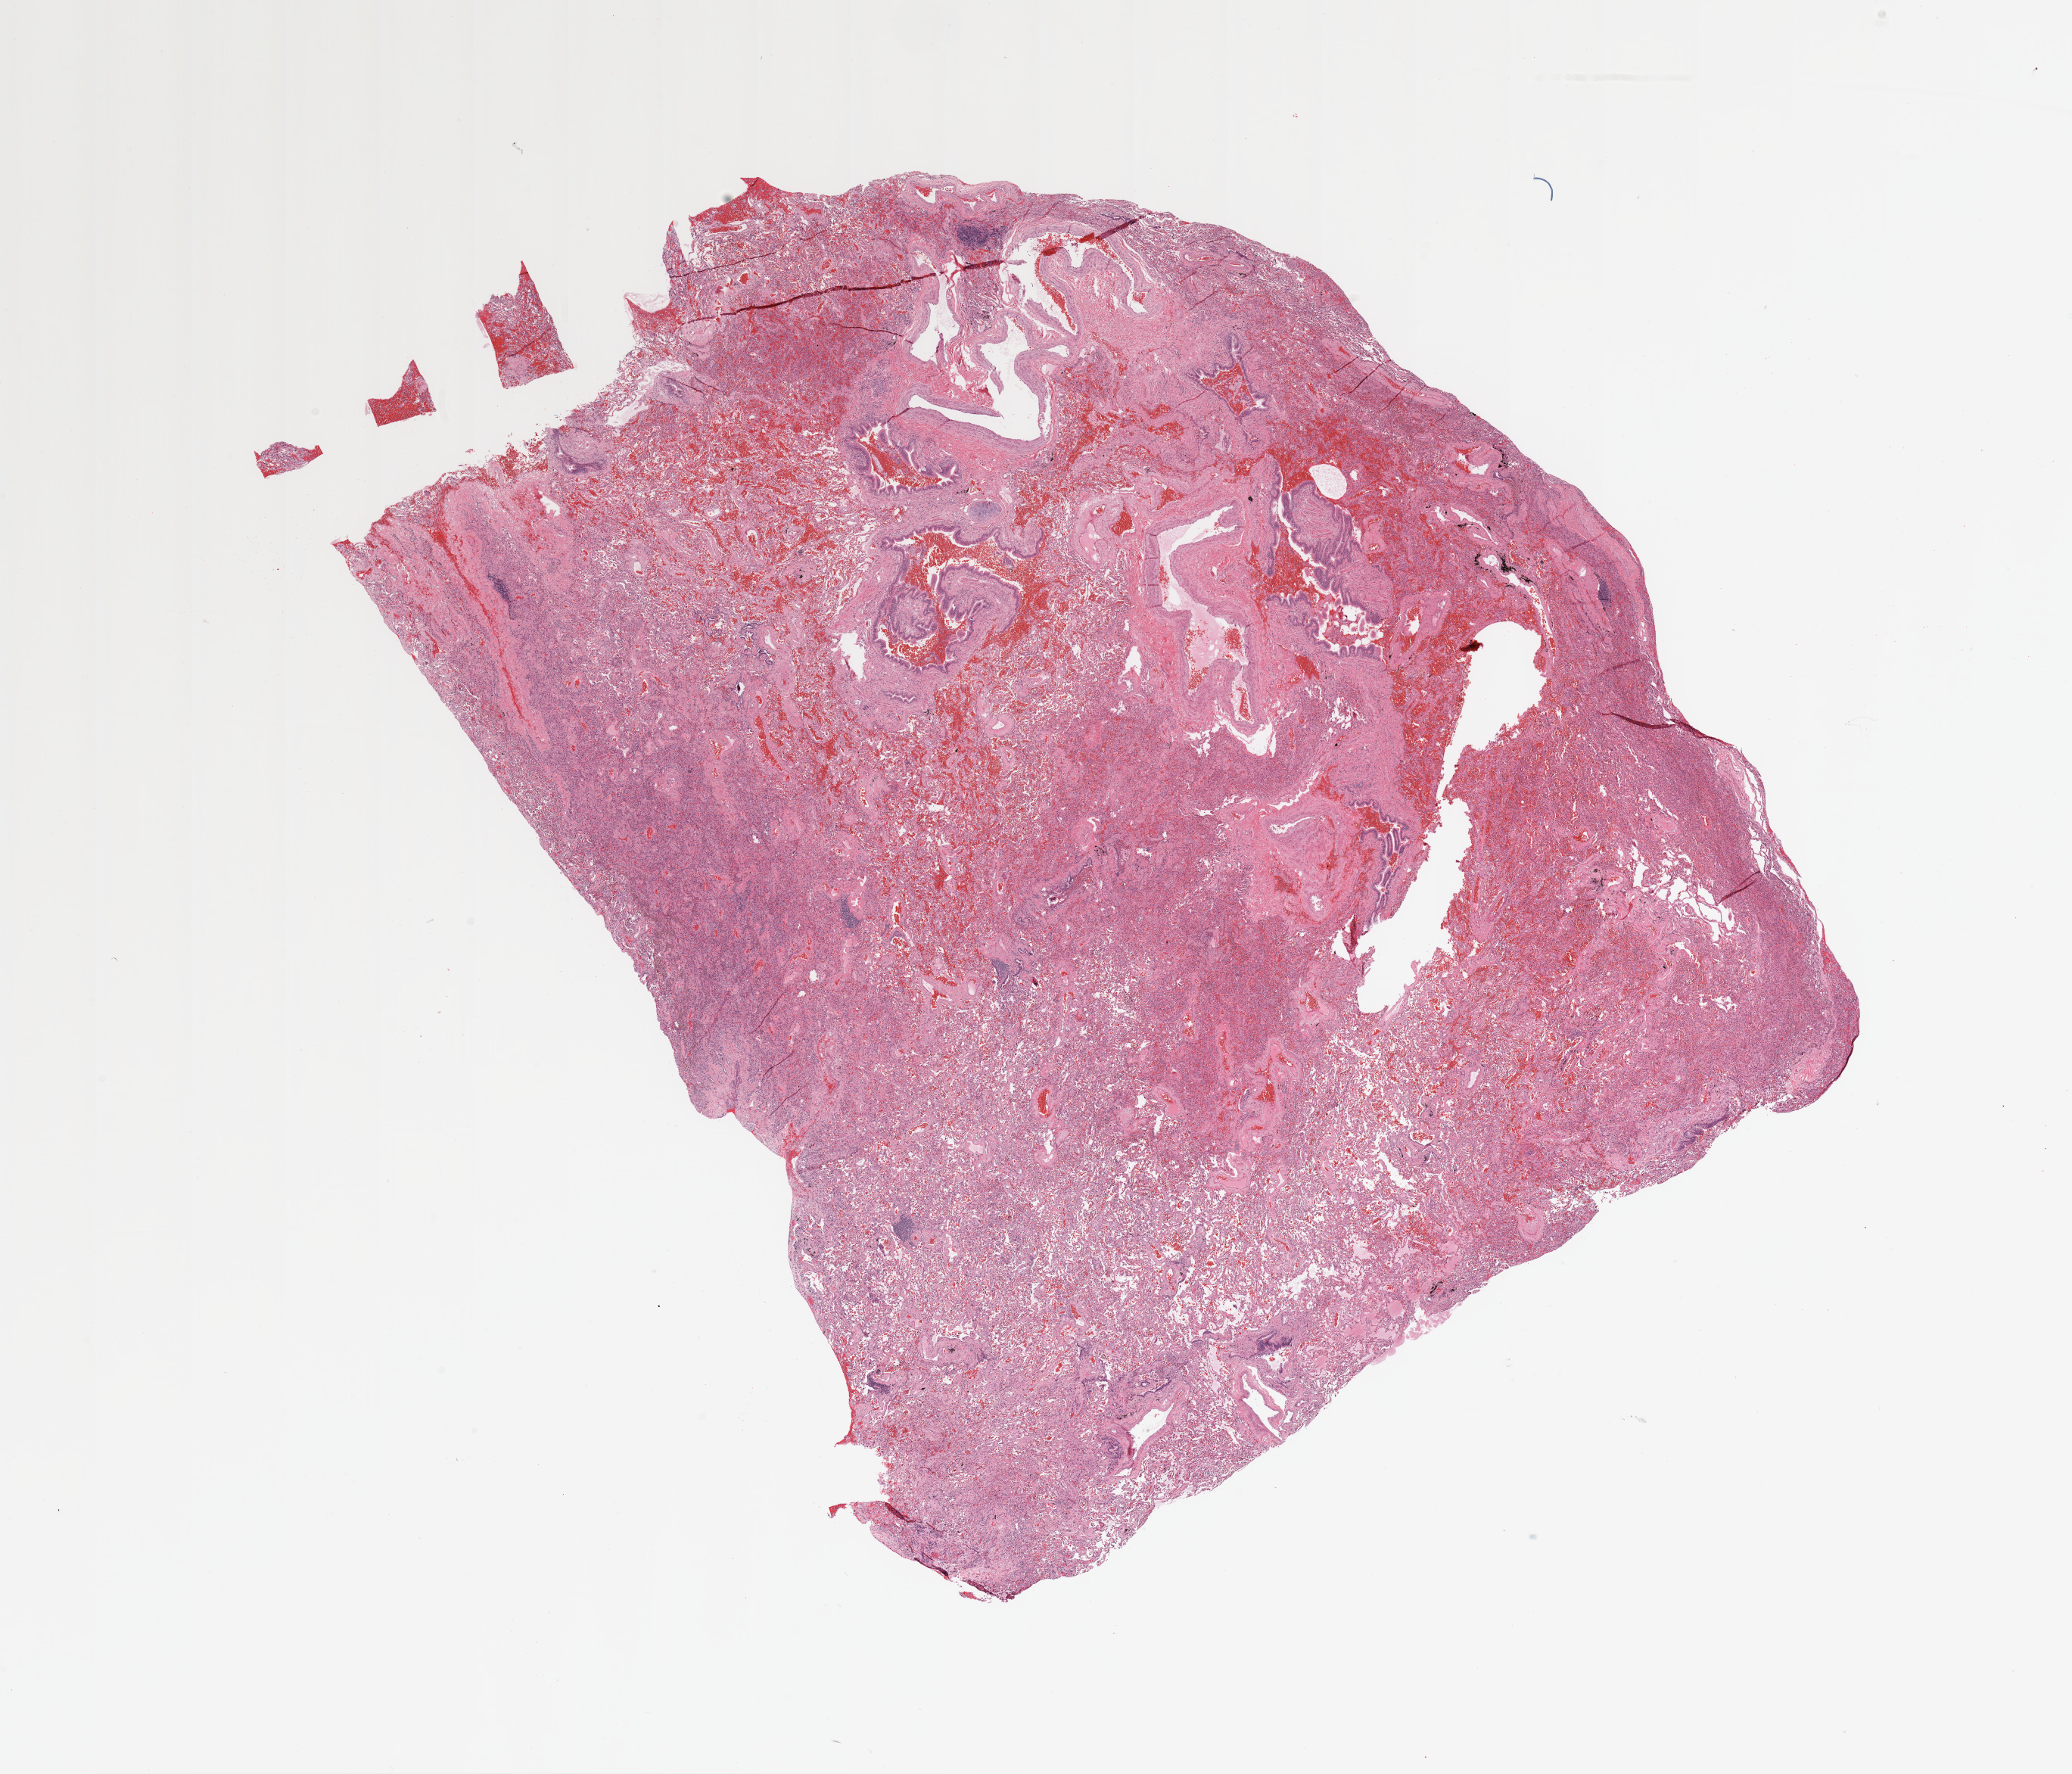
Whole-slide histology image, Hematoxylin and eosin (H&E) stained — whole scanned area (about 21.7 x 18.5 mm) shown as a low-resolution overview, normal (non-tumour) tissue sample, sampled site: lung. Patient: male, age 71 years.
- this section: normal (non-tumour) tissue from the same patient
- patient diagnosis: Adenocarcinoma, NOS